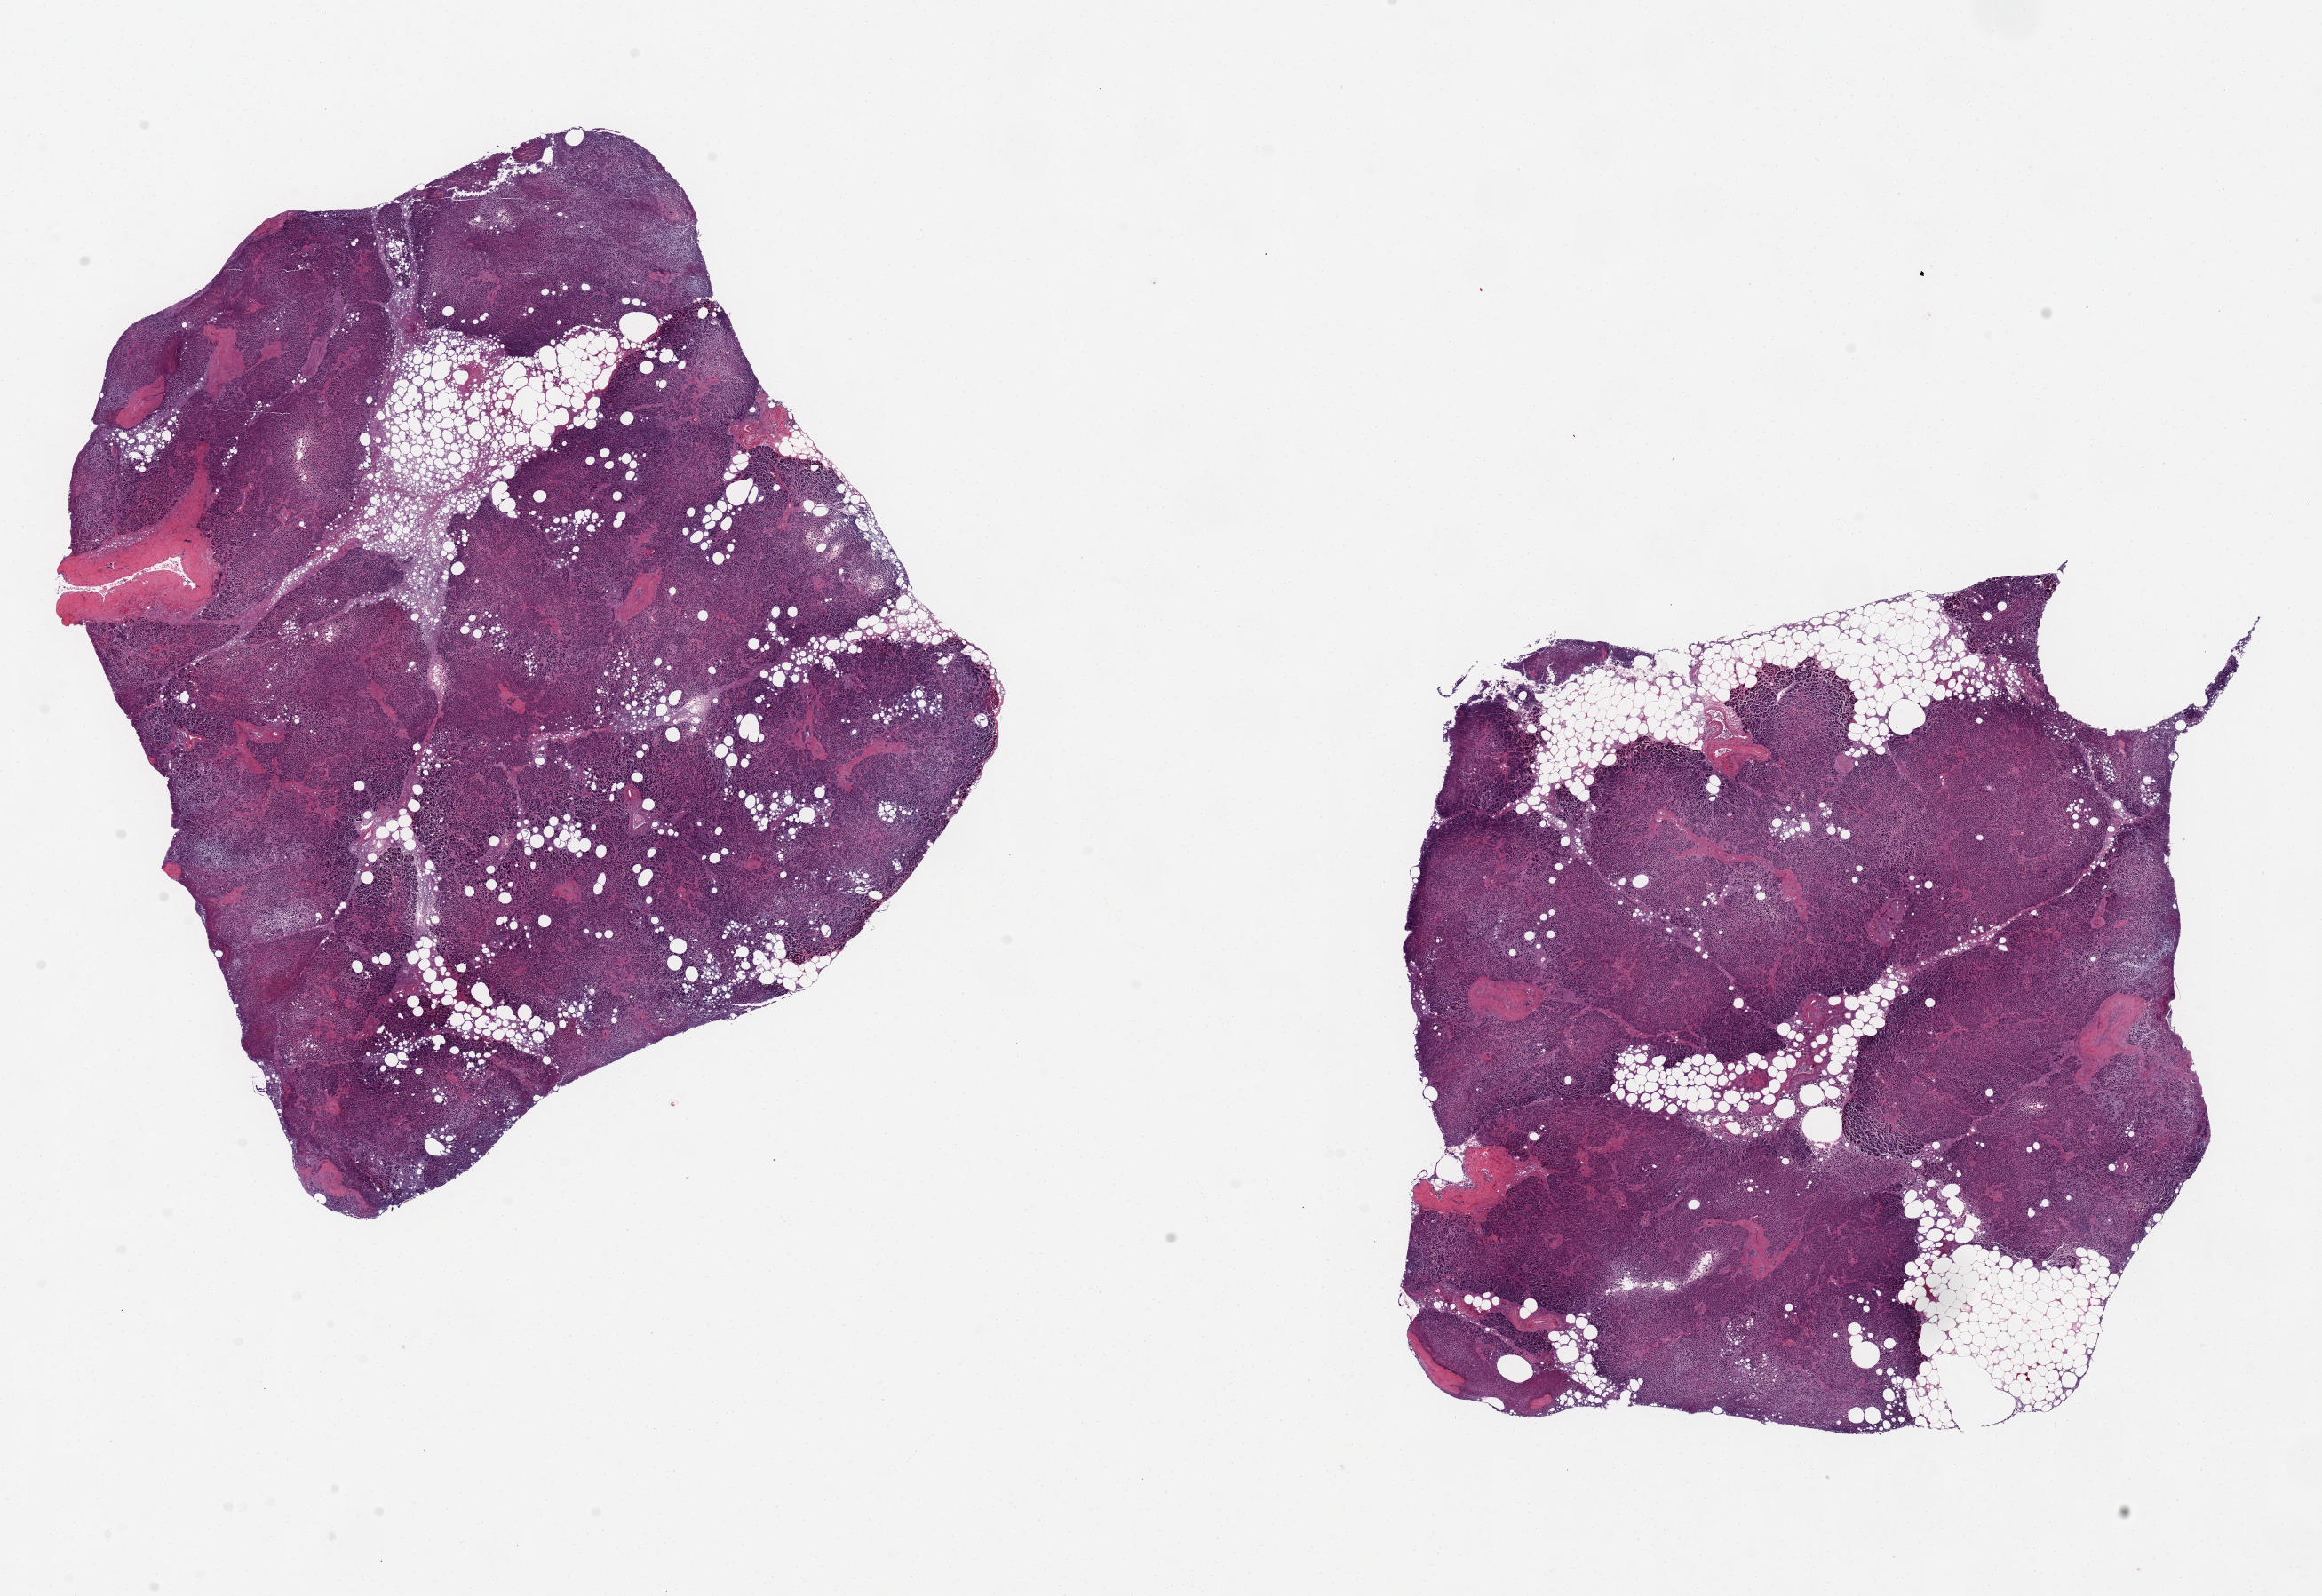
Hematoxylin and eosin (H&E) whole-slide image, low-resolution overview of the scanned area, about 20.7 x 14.2 mm (slide scanned at 20x). PAXgene-fixed, paraffin-embedded tissue. Section of pancreas (target tissue). Tissue donor sample. Donor: male.
• pathologist's review note for this sample: 2 aliquots, ~8x7mm. ~20% interstital fat, marked saponification/autolysis